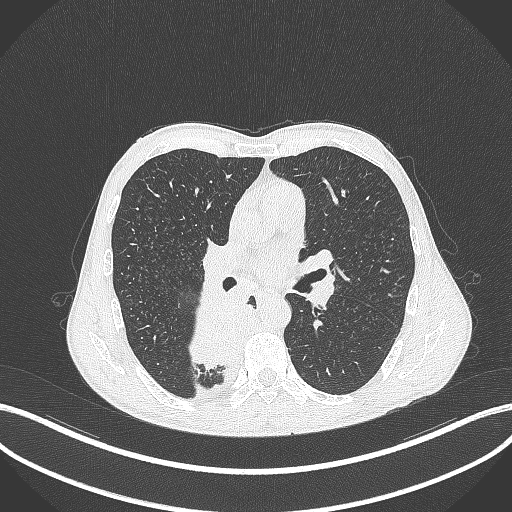
Chest CT, one axial slice. Slice 209 of 371 in the series (ordered by position). Reconstruction kernel B70f. 120 kVp. Lung window (W 1500 / L -600 HU). 512 × 512 image matrix, field of view 400 × 400 mm. Patient: male, 58 years. Case-level facts recorded for this patient, not image findings: clinical TNM (as recorded): T3 N1 M1.
Structures marked on this image (bounding box drawn by a radiologist):
- lung tumour (recorded histology: squamous cell carcinoma): bounding box (x1, y1, x2, y2) in pixels: (189, 284, 244, 371)